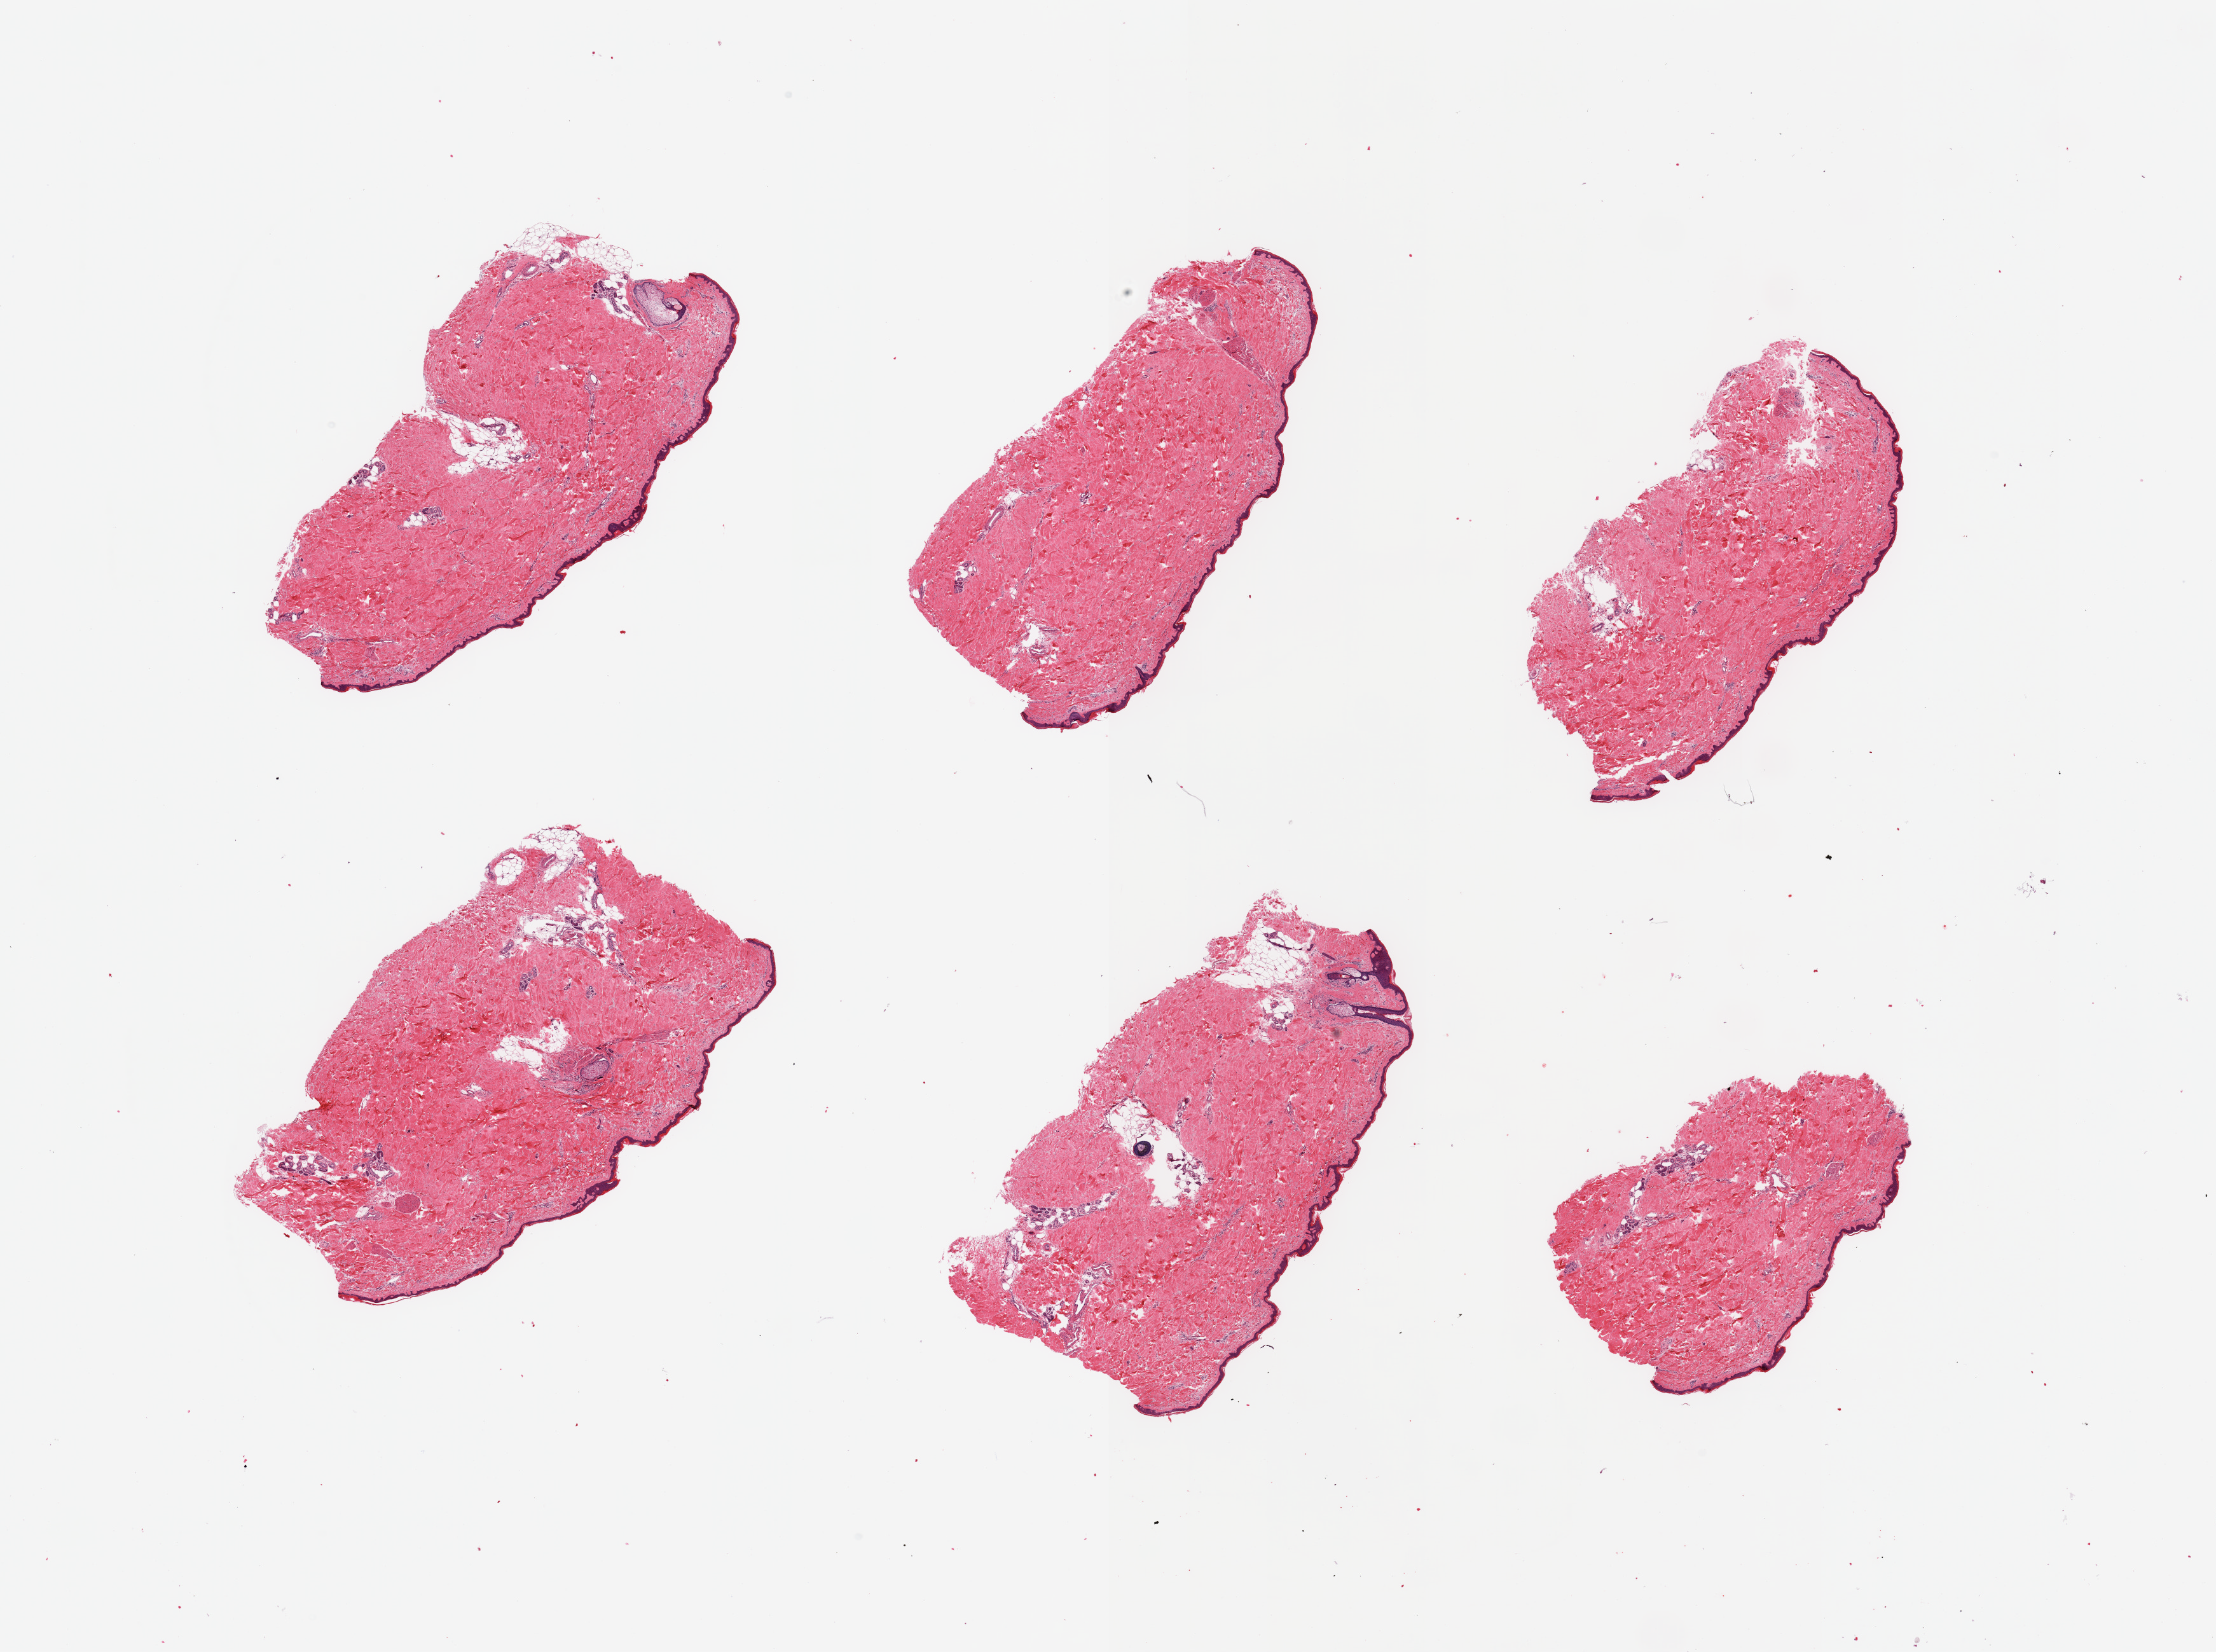
H&E whole-slide image, brightfield — low-resolution overview of the scanned area, about 27.6 x 20.5 mm (acquisition: 20x scan). PAXgene-fixed paraffin-embedded (PFPE) section. Target tissue: skin of lower leg. Donor tissue sample. Male donor.
Reviewer comment on this tissue sample: 6 pieces; well trimmed; up to 10% dermal fat.